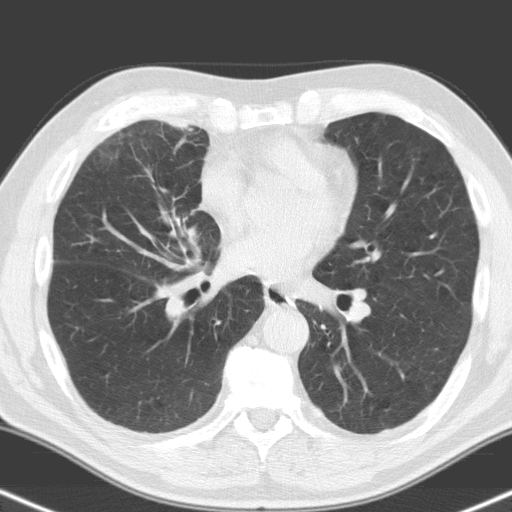
Low-dose screening chest CT, one axial slice. 120 kVp. Lung window (W 1500 / L -600 HU). 3.2 mm slice thickness. 512 × 512 image matrix, field of view 324 × 324 mm.
Outlined on this slice (expert manual segmentation):
- lesion 1 (tumor, hilum of right lung): bounding box <167,272,215,319> (left, top, right, bottom; pixels)